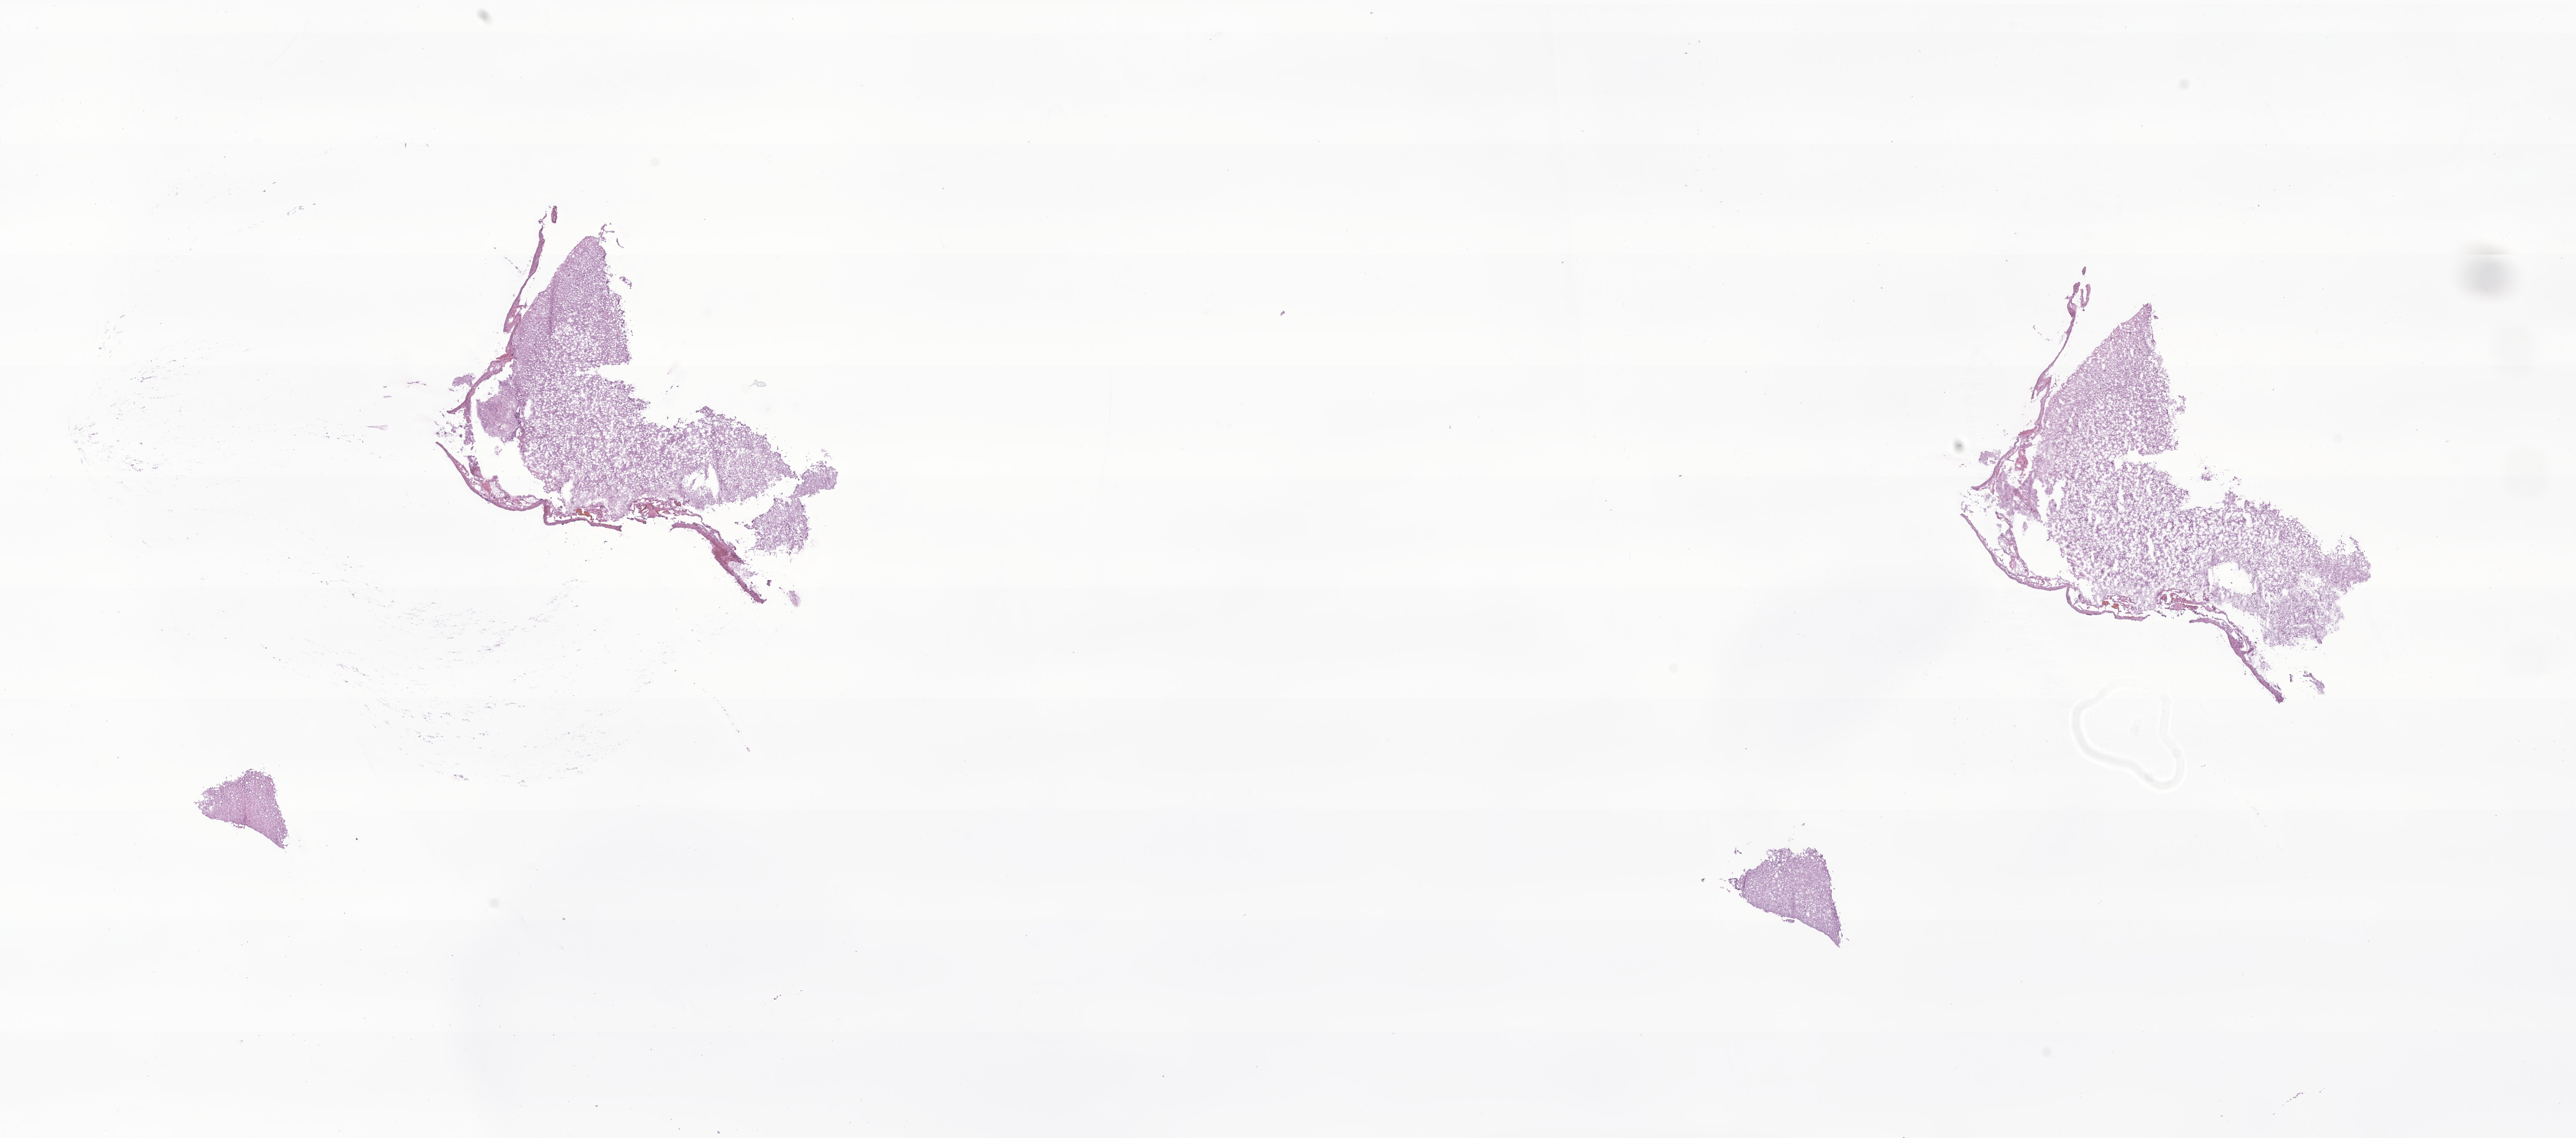
Digitized H&E-stained section of tumor tissue from the temporal lobe, shown as a low-resolution overview of the whole scanned area (about 24.8 x 11.0 mm). Cryosection (OCT / tissue freezing medium). Female patient, age 218 months (18 years 2 months).
* diagnosis (ICD-O-3 morphology term): Ganglioglioma, NOS